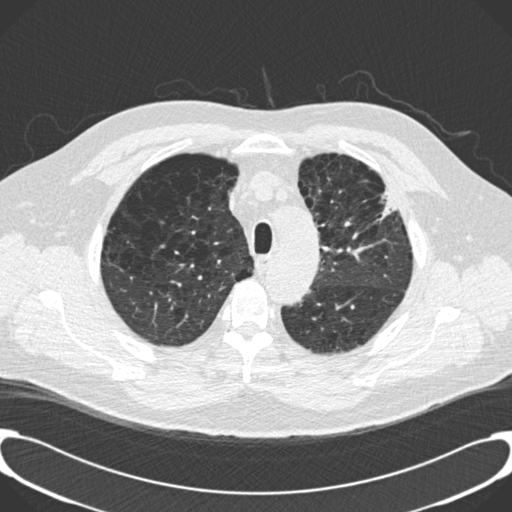
Low-dose screening chest CT, one axial slice; position 155 of 189 along the scan axis; reconstruction kernel B30f; 120 kVp; lung window (W 1500 / L -600 HU); 2 mm slice thickness; 512 × 512 image matrix.
Structures marked on this image (expert manual segmentation):
- lesion 1 (tumor, upper lobe of left lung): bounding box (x1, y1, x2, y2) in pixels: (379, 190, 398, 220)